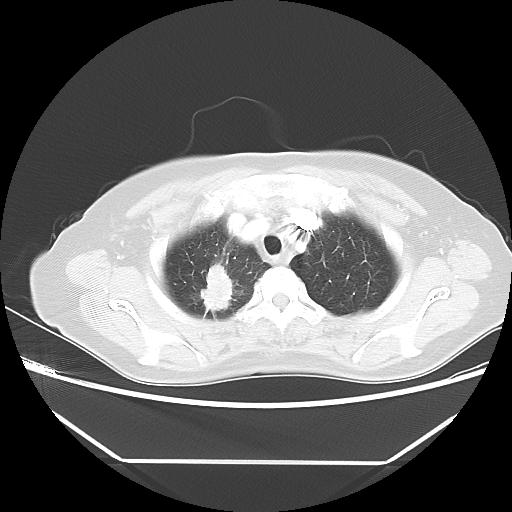
Chest CT, one axial slice. Reconstruction kernel LUNG. Lung window (W 1500 / L -600 HU). 5 mm slice thickness. 512 × 512 image matrix, field of view 360 × 360 mm. Patient: female, 65 years. Case-level facts recorded for this patient, not image findings: clinical TNM (as recorded): T1c N1 M1.
Annotated regions visible in this slice (bounding box drawn by a radiologist):
- lung tumour (recorded histology: adenocarcinoma): box from (x=201, y=262) to (x=239, y=315) px